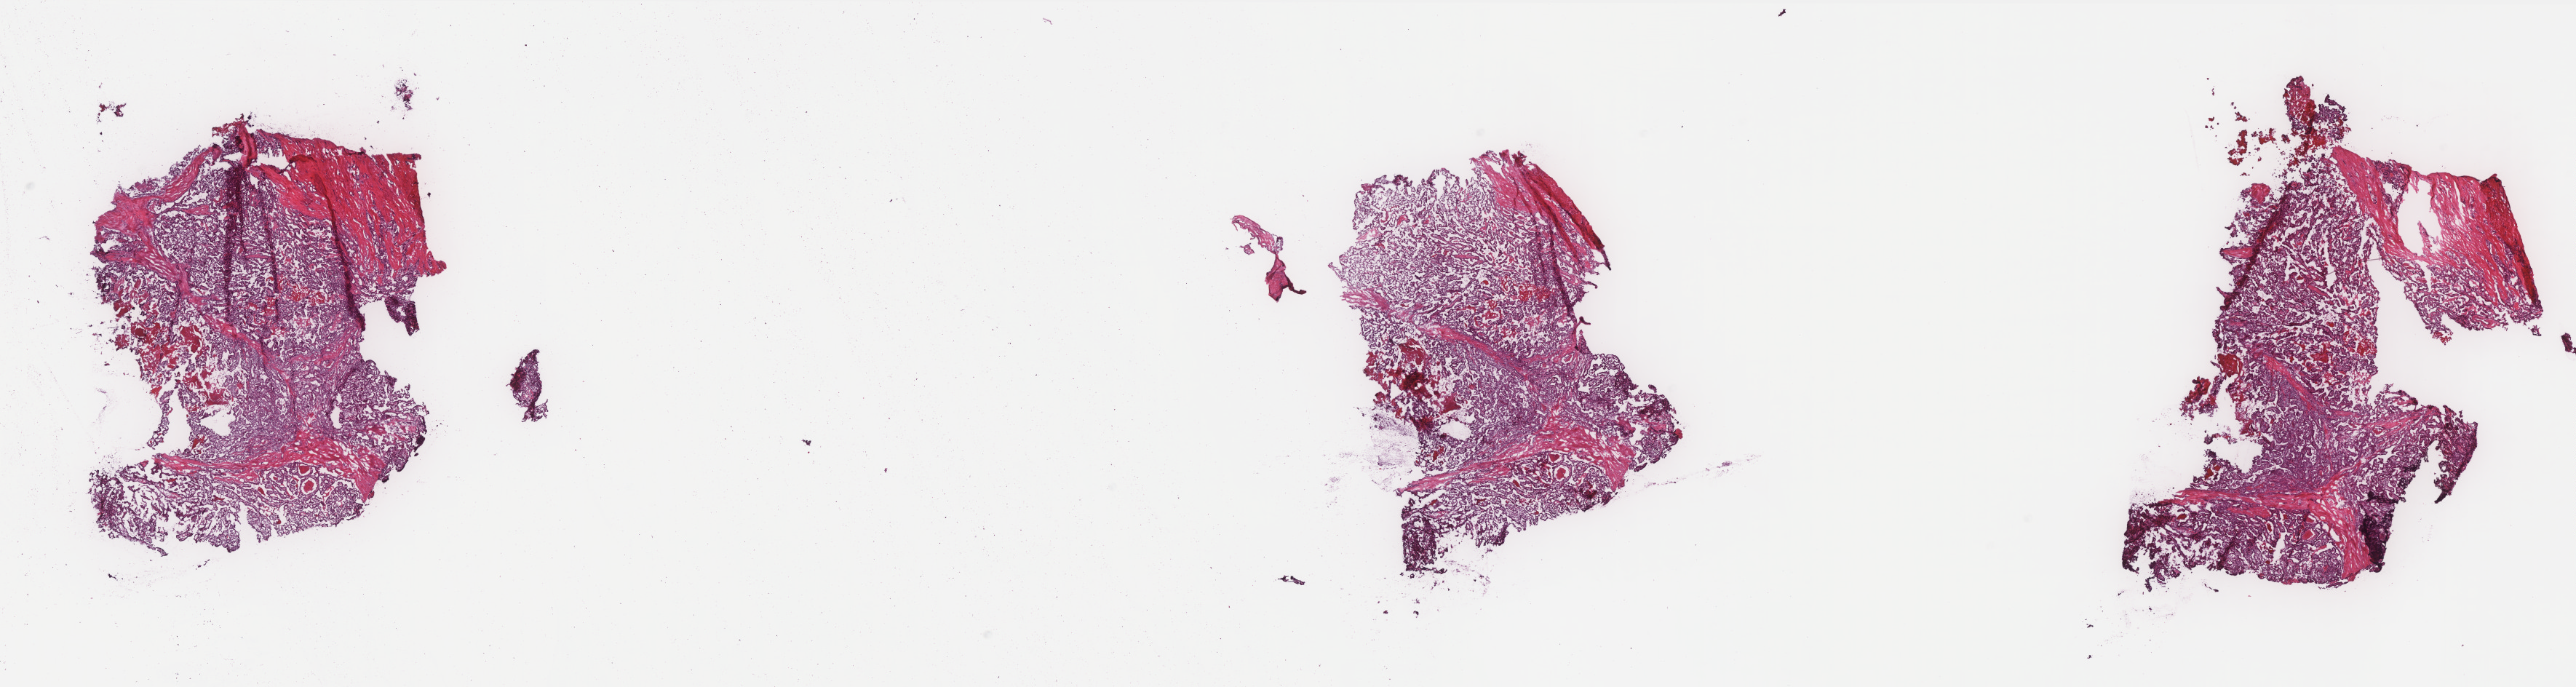
Digitized H&E-stained tissue section (whole slide), a low-resolution overview of the entire scanned area, about 28.4 x 7.6 mm (slide scanned at 40x), frozen section from the top of the tissue portion, primary tumour sample from the thyroid. Male, age 76 years at initial diagnosis. Pathologist review of this section (percent, as recorded): tumour cells 95%, tumour nuclei 93%, normal cells 0%, stromal cells 5%, necrosis 0%. Inflammatory infiltration, as recorded: lymphocyte infiltration 0%, monocyte infiltration 0%, neutrophil infiltration 0%.
Lymph nodes positive (case pathology): 1 of 22 examined. AJCC pathologic stage: IVA. Diagnosis: Papillary adenocarcinoma, NOS (thyroid gland).